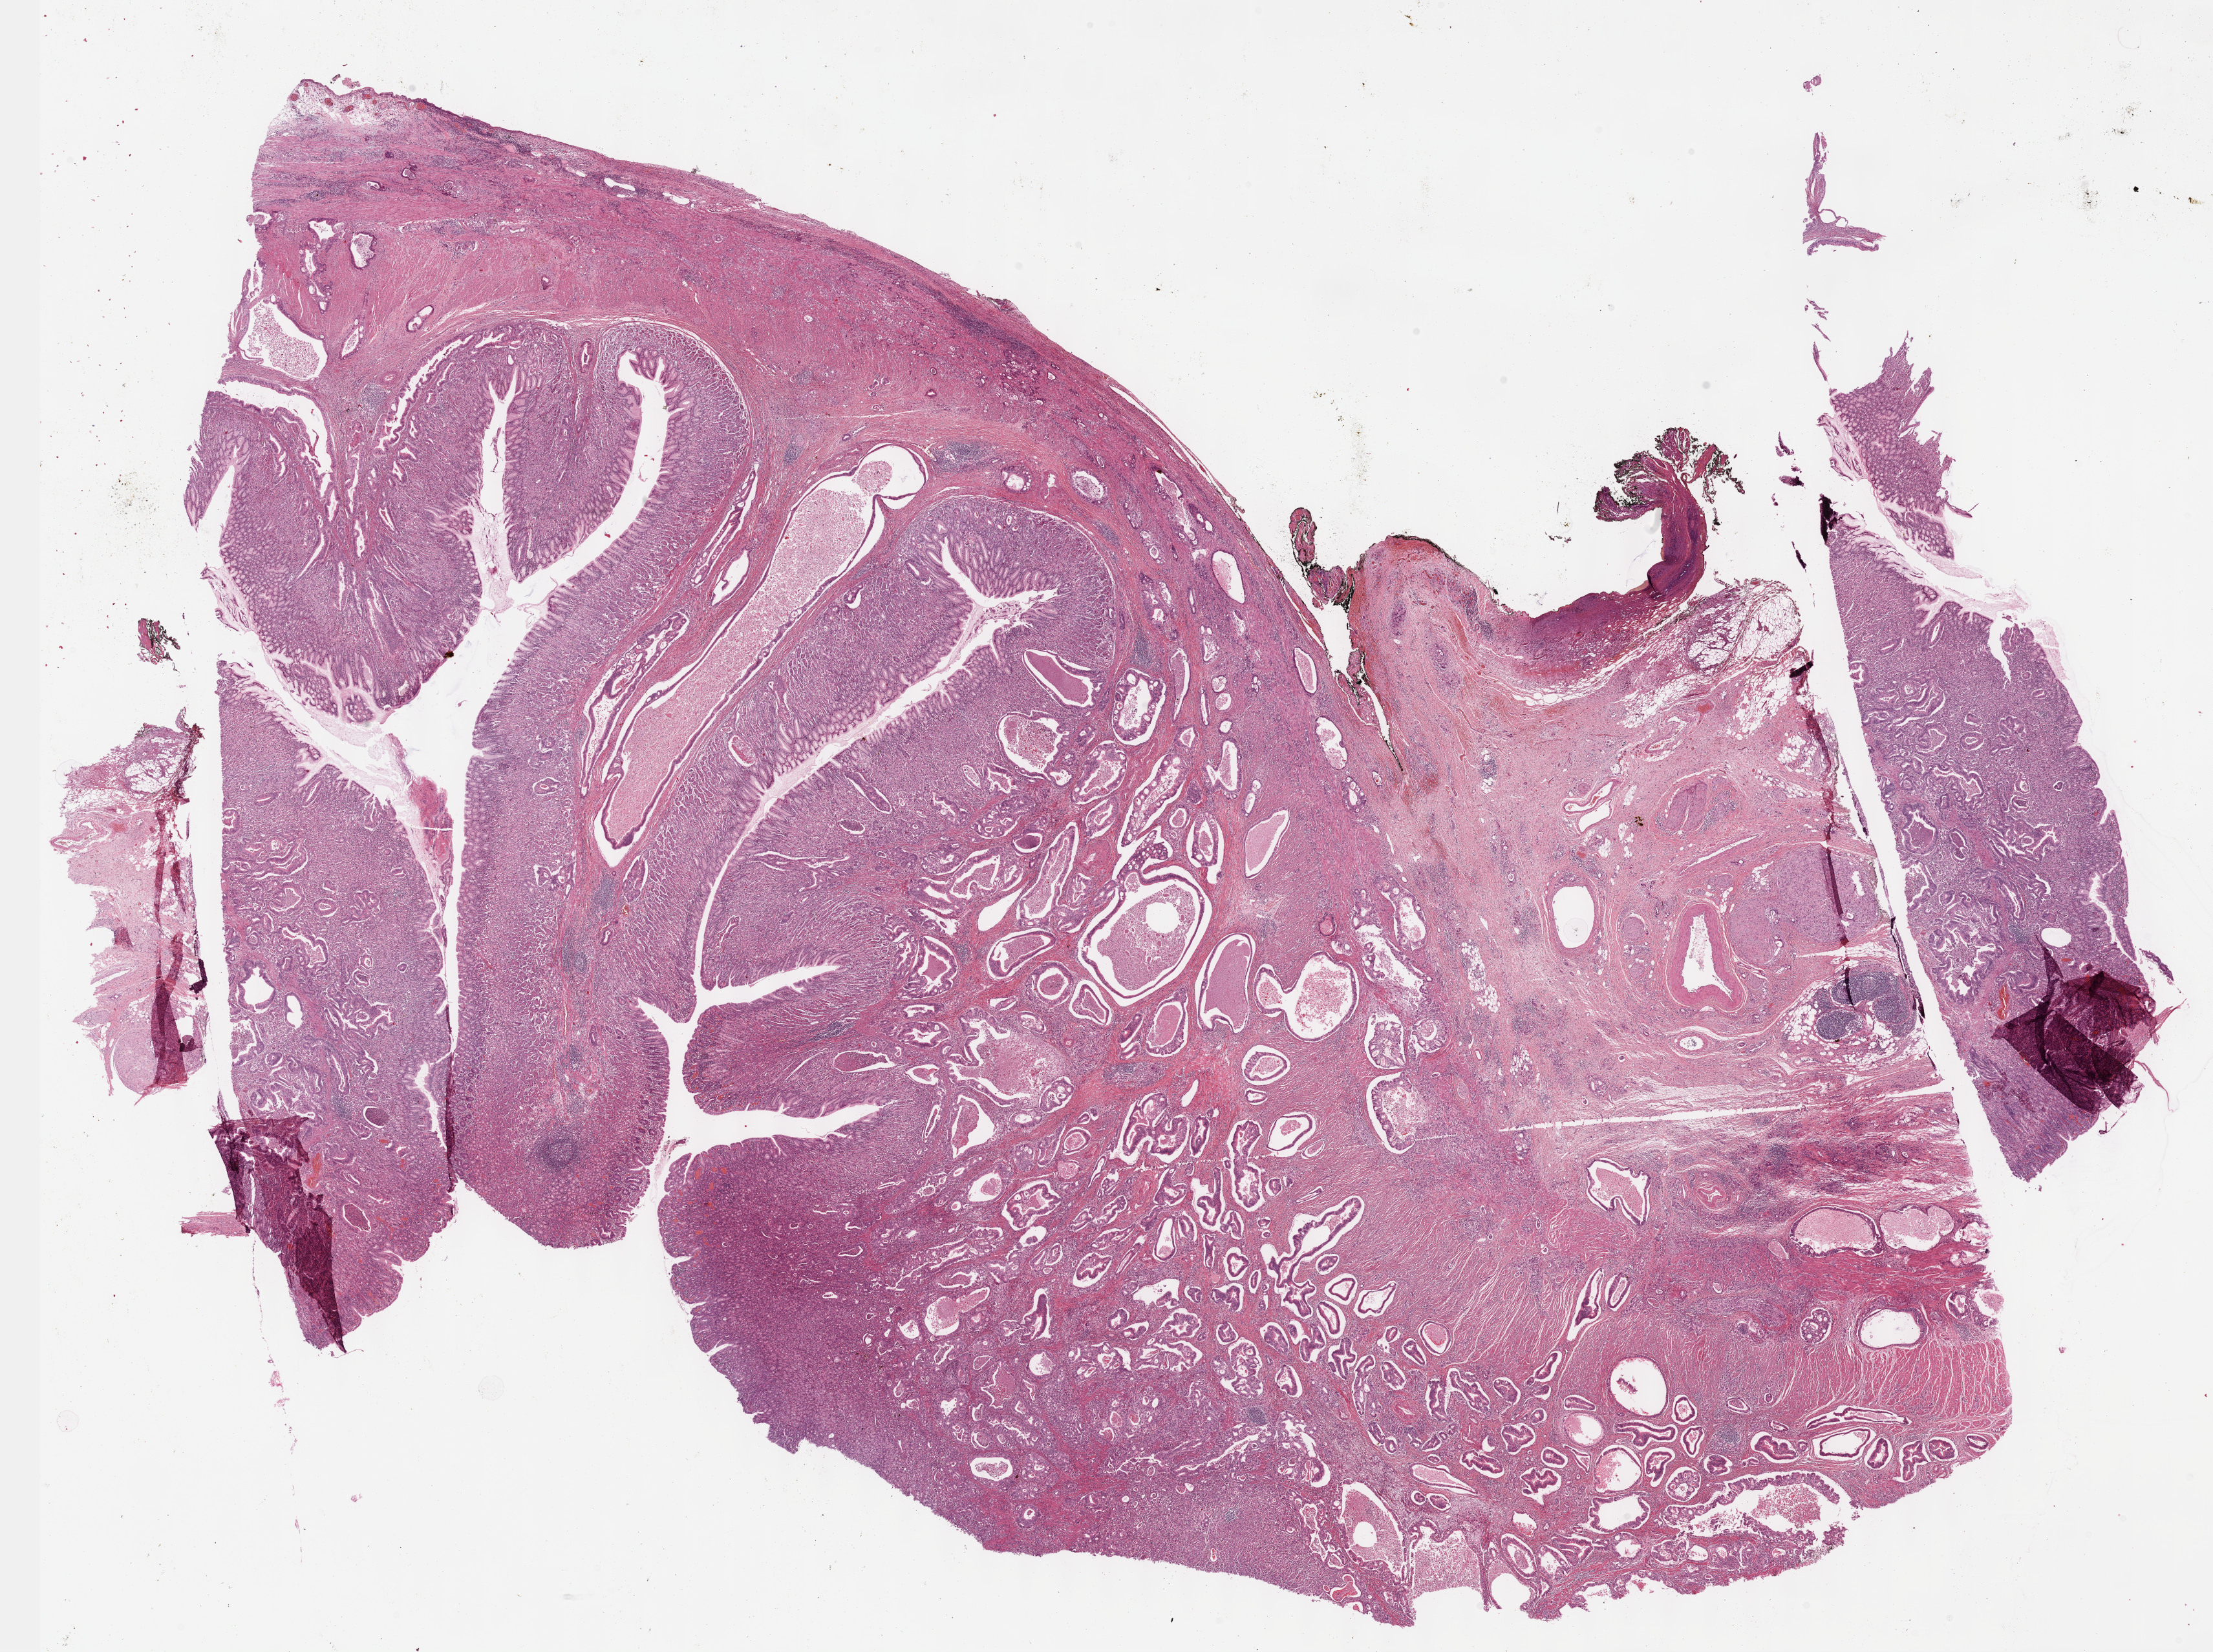
Whole-slide histology image, H&E — shown as a low-resolution overview of the whole scanned area (about 27.7 x 20.7 mm, acquisition: 40x scan). Formalin-fixed paraffin-embedded (FFPE) diagnostic section. Primary tumour sample from the stomach. Patient: female, age at initial diagnosis 50 years. Histologic grade: G2 (moderately differentiated).
Lymph nodes positive (case pathology): 6 of 12 examined. AJCC pathologic stage: IV (6th edition). Pathologic diagnosis: Tubular adenocarcinoma (cardia, NOS).